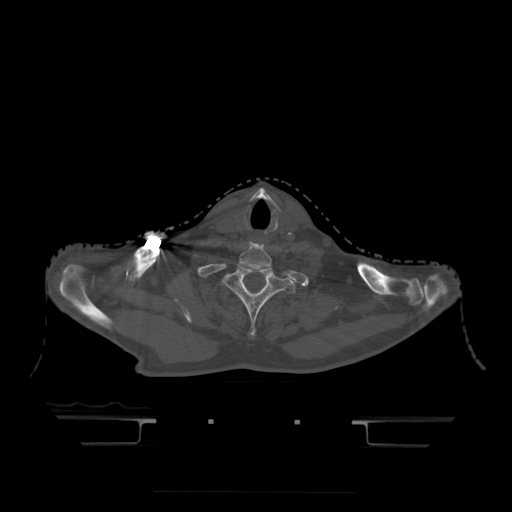
CT including the spine, one axial slice; position 400 of 522 along the scan axis; bone window (W 1800 / L 400 HU); 1.25 mm slice thickness; 512 × 512 image matrix. Patient age 68 years. Case-level facts recorded for this patient, not image findings: primary cancer: urothelial.
Structures marked on this image (semi-automatic segmentation, software-assisted and operator-edited):
- T1 vertebra: bounding box [x1, y1, x2, y2] px = [225, 266, 295, 335]